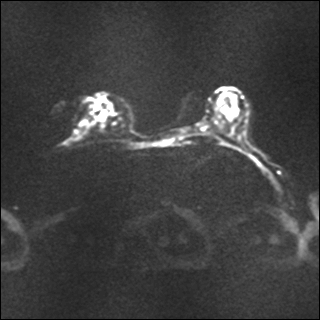
Breast MRI, one axial slice. Slice 15 of 35 in the series (ordered by position). Diffusion-weighted series; image 2 of 4 stored at this slice position (different b-values; order by instance number). 1.5 T. 4 mm slice thickness. 320 × 320 image matrix. Female patient.
Annotated regions visible in this slice (manually delineated by an expert):
- tumour on diffusion-weighted imaging: bounding box (x1, y1, x2, y2) in pixels: (94, 104, 101, 123)